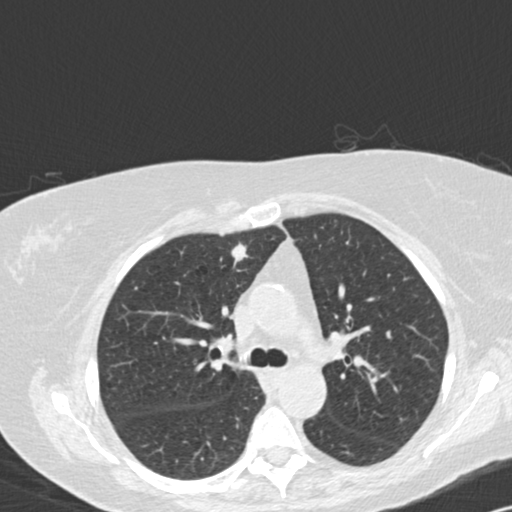
Low-dose screening chest CT, one axial slice. Position 97 of 141 along the scan axis. Lung window (W 1500 / L -600 HU). 512 × 512 image matrix.
Outlined on this slice (manually delineated by an expert):
- lesion 1 (tumor, upper lobe of right lung): box from (x=231, y=243) to (x=248, y=263) px